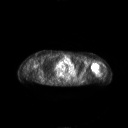
FDG PET of an extremity soft-tissue mass (from a PET/CT study), one axial slice. Position 182 of 267 along the scan axis. 3.27 mm slice thickness. 128 × 128 image matrix, field of view 700 × 700 mm. Patient: female, 83 years. Case-level facts recorded for this patient, not image findings: histological type: pleiomorphic leiomyosarcoma; grade: high; site of the primary tumour: left biceps.
Annotated regions visible in this slice (expert contour drawn on MRI and transferred to this co-registered scan by the dataset authors):
- gross tumour volume including surrounding oedema: box from (x=91, y=63) to (x=99, y=74) px
- gross tumour volume (mass): (x=91, y=63)–(x=99, y=72)